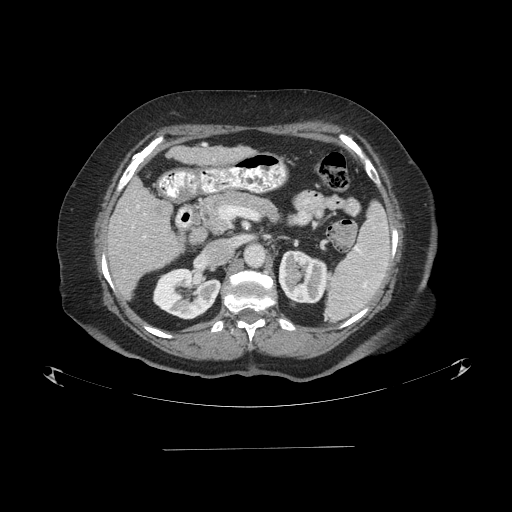
Contrast-enhanced abdominal CT (liver protocol), one axial slice; position 41 of 103 along the scan axis; reconstruction kernel STANDARD; 120 kVp; one of 2 acquisitions stored at this slice position; soft-tissue window (W 400 / L 40 HU); 2.5 mm slice thickness; 512 × 512 image matrix, field of view 500 × 500 mm. From the clinical record (not read from this slice): diagnosis: hepatocellular carcinoma (patient treated with transarterial chemoembolisation; whether this scan precedes or follows treatment is not stated here); TNM stage (as recorded): Stage-IIIA; Child-Pugh class: A; tumour size: 5.2 cm.
Outlined on this slice (semi-automatically segmented with operator editing):
- liver parenchyma outside the tumour (the mass and vessels are separate outlines, so this box may not span the whole liver): bounding box [x1, y1, x2, y2] px = [106, 178, 182, 298]
- liver vessels: [137, 205, 145, 238]